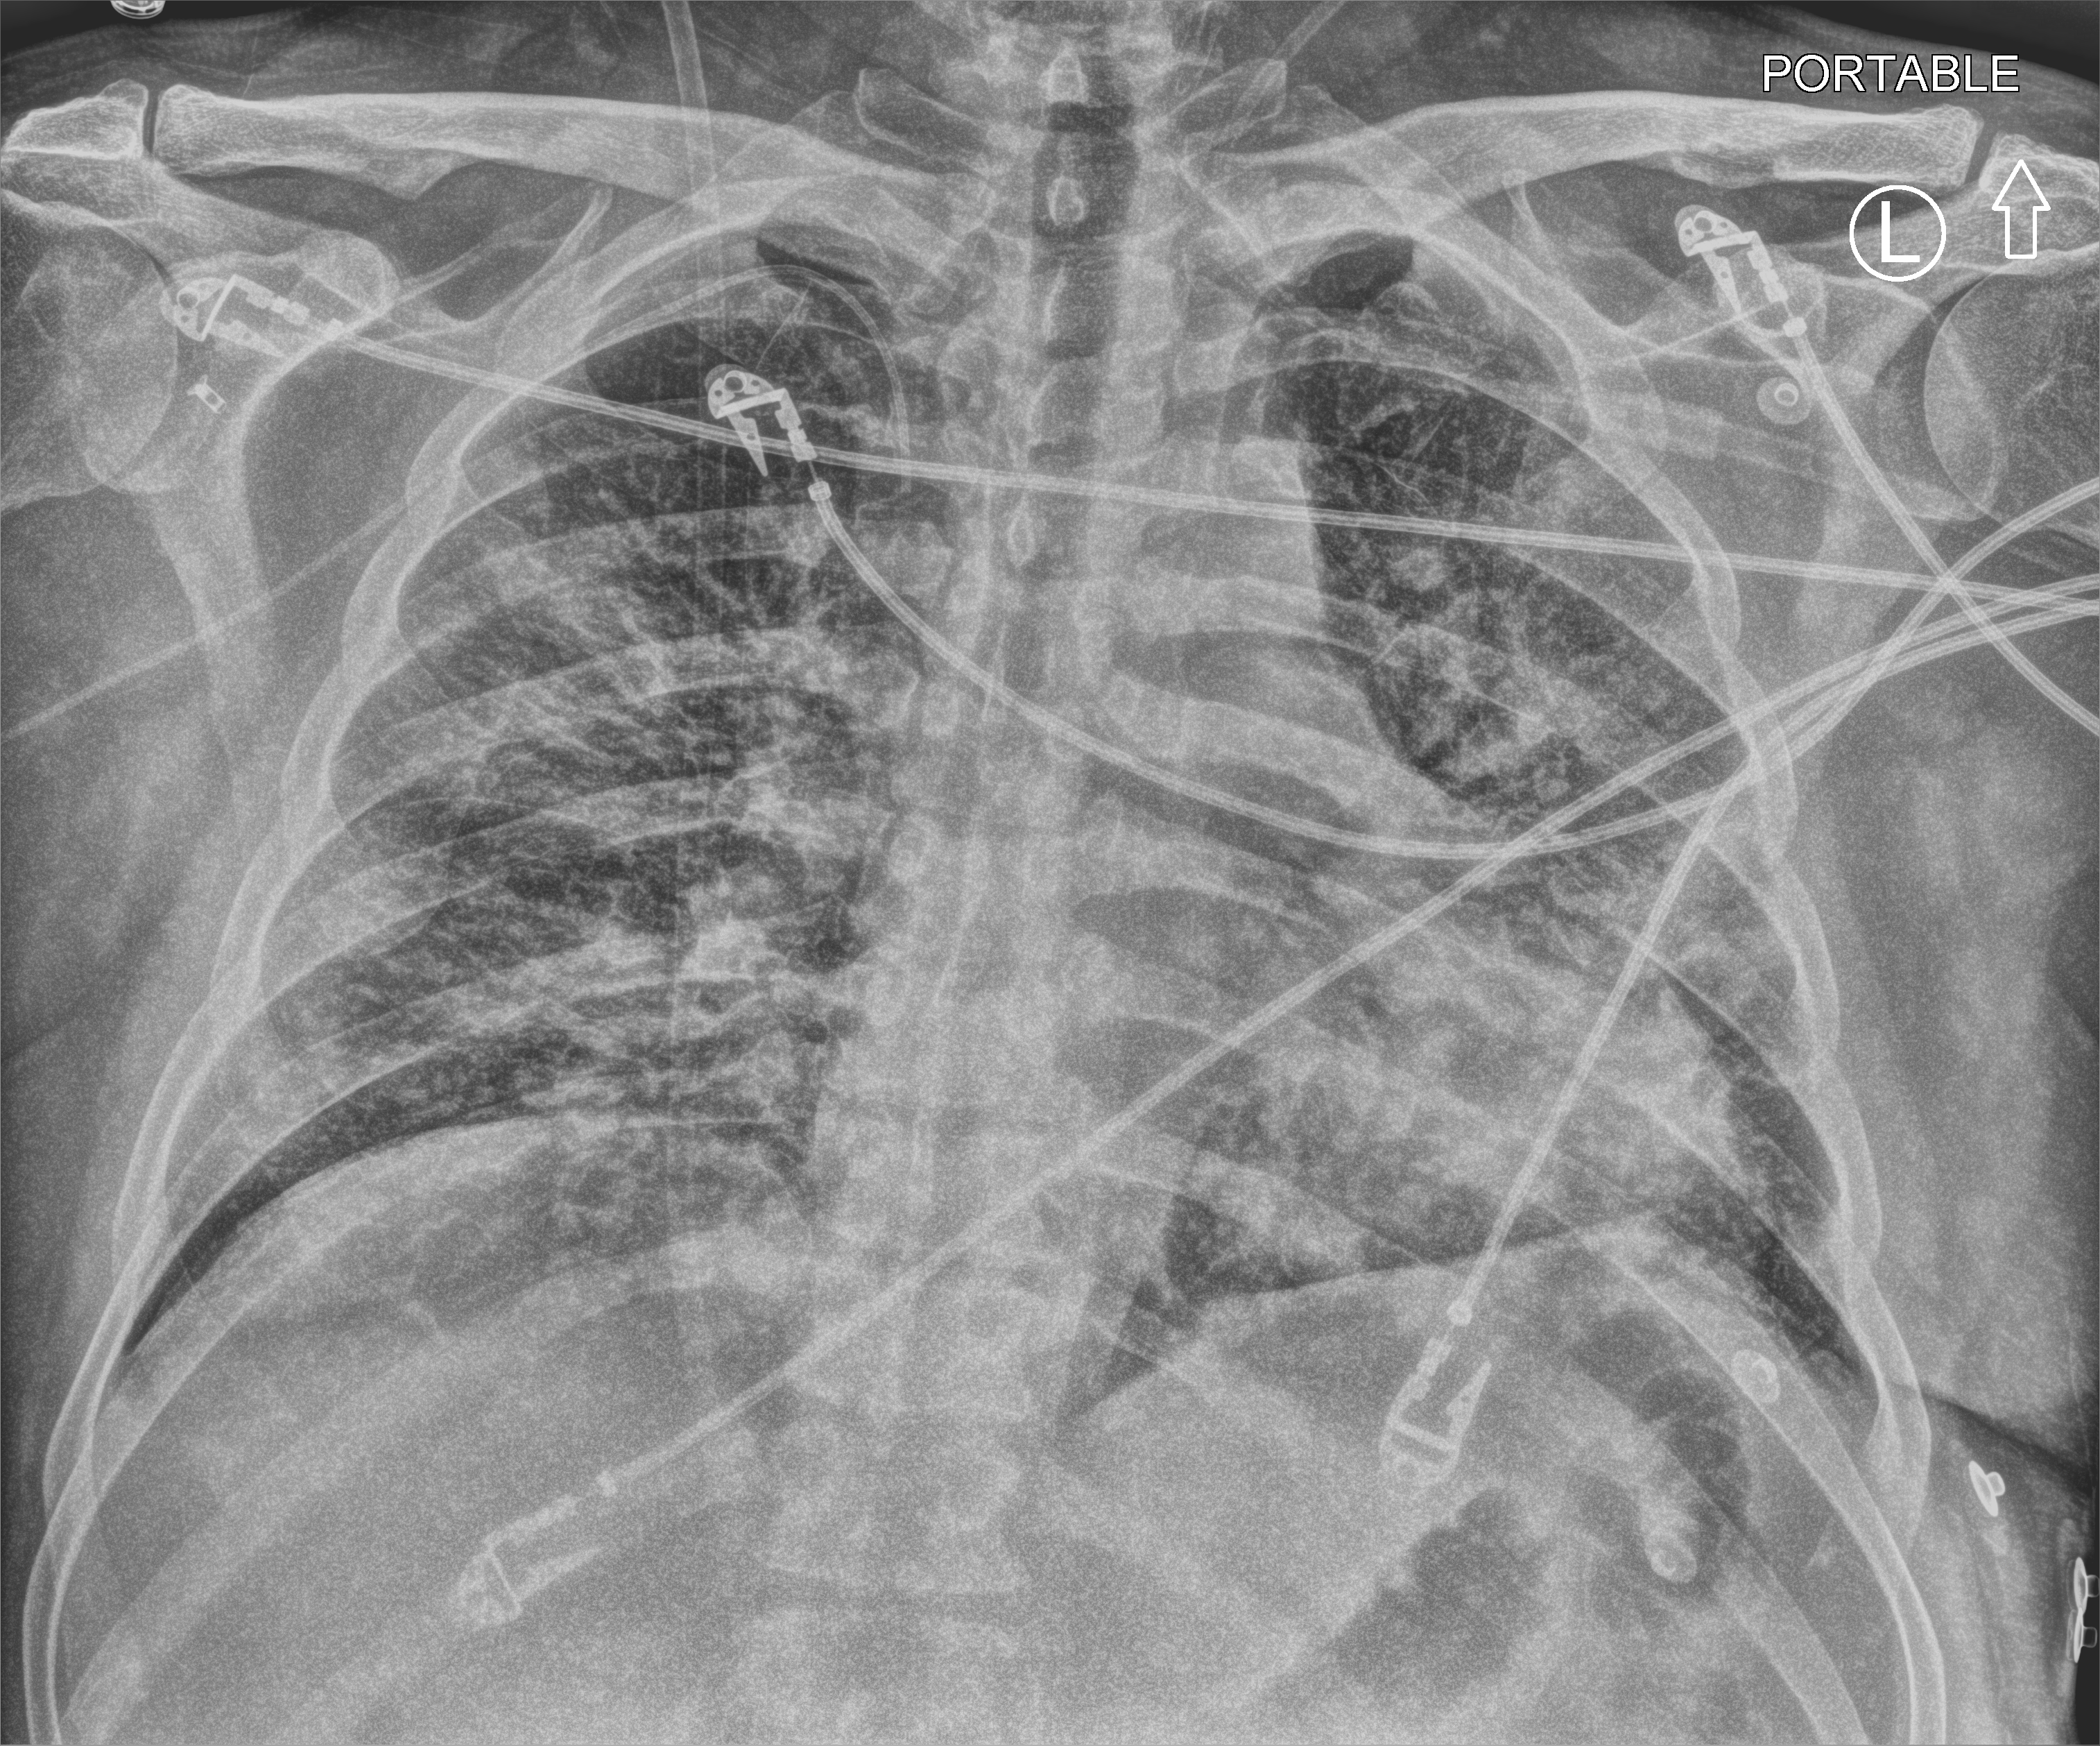
Portable chest radiograph. Patient hospitalised with COVID-19; male, aged 18–59 years.
Admission-level facts for this patient (not findings on this image; timing relative to this image not recorded): mechanically ventilated during this hospital stay: yes.